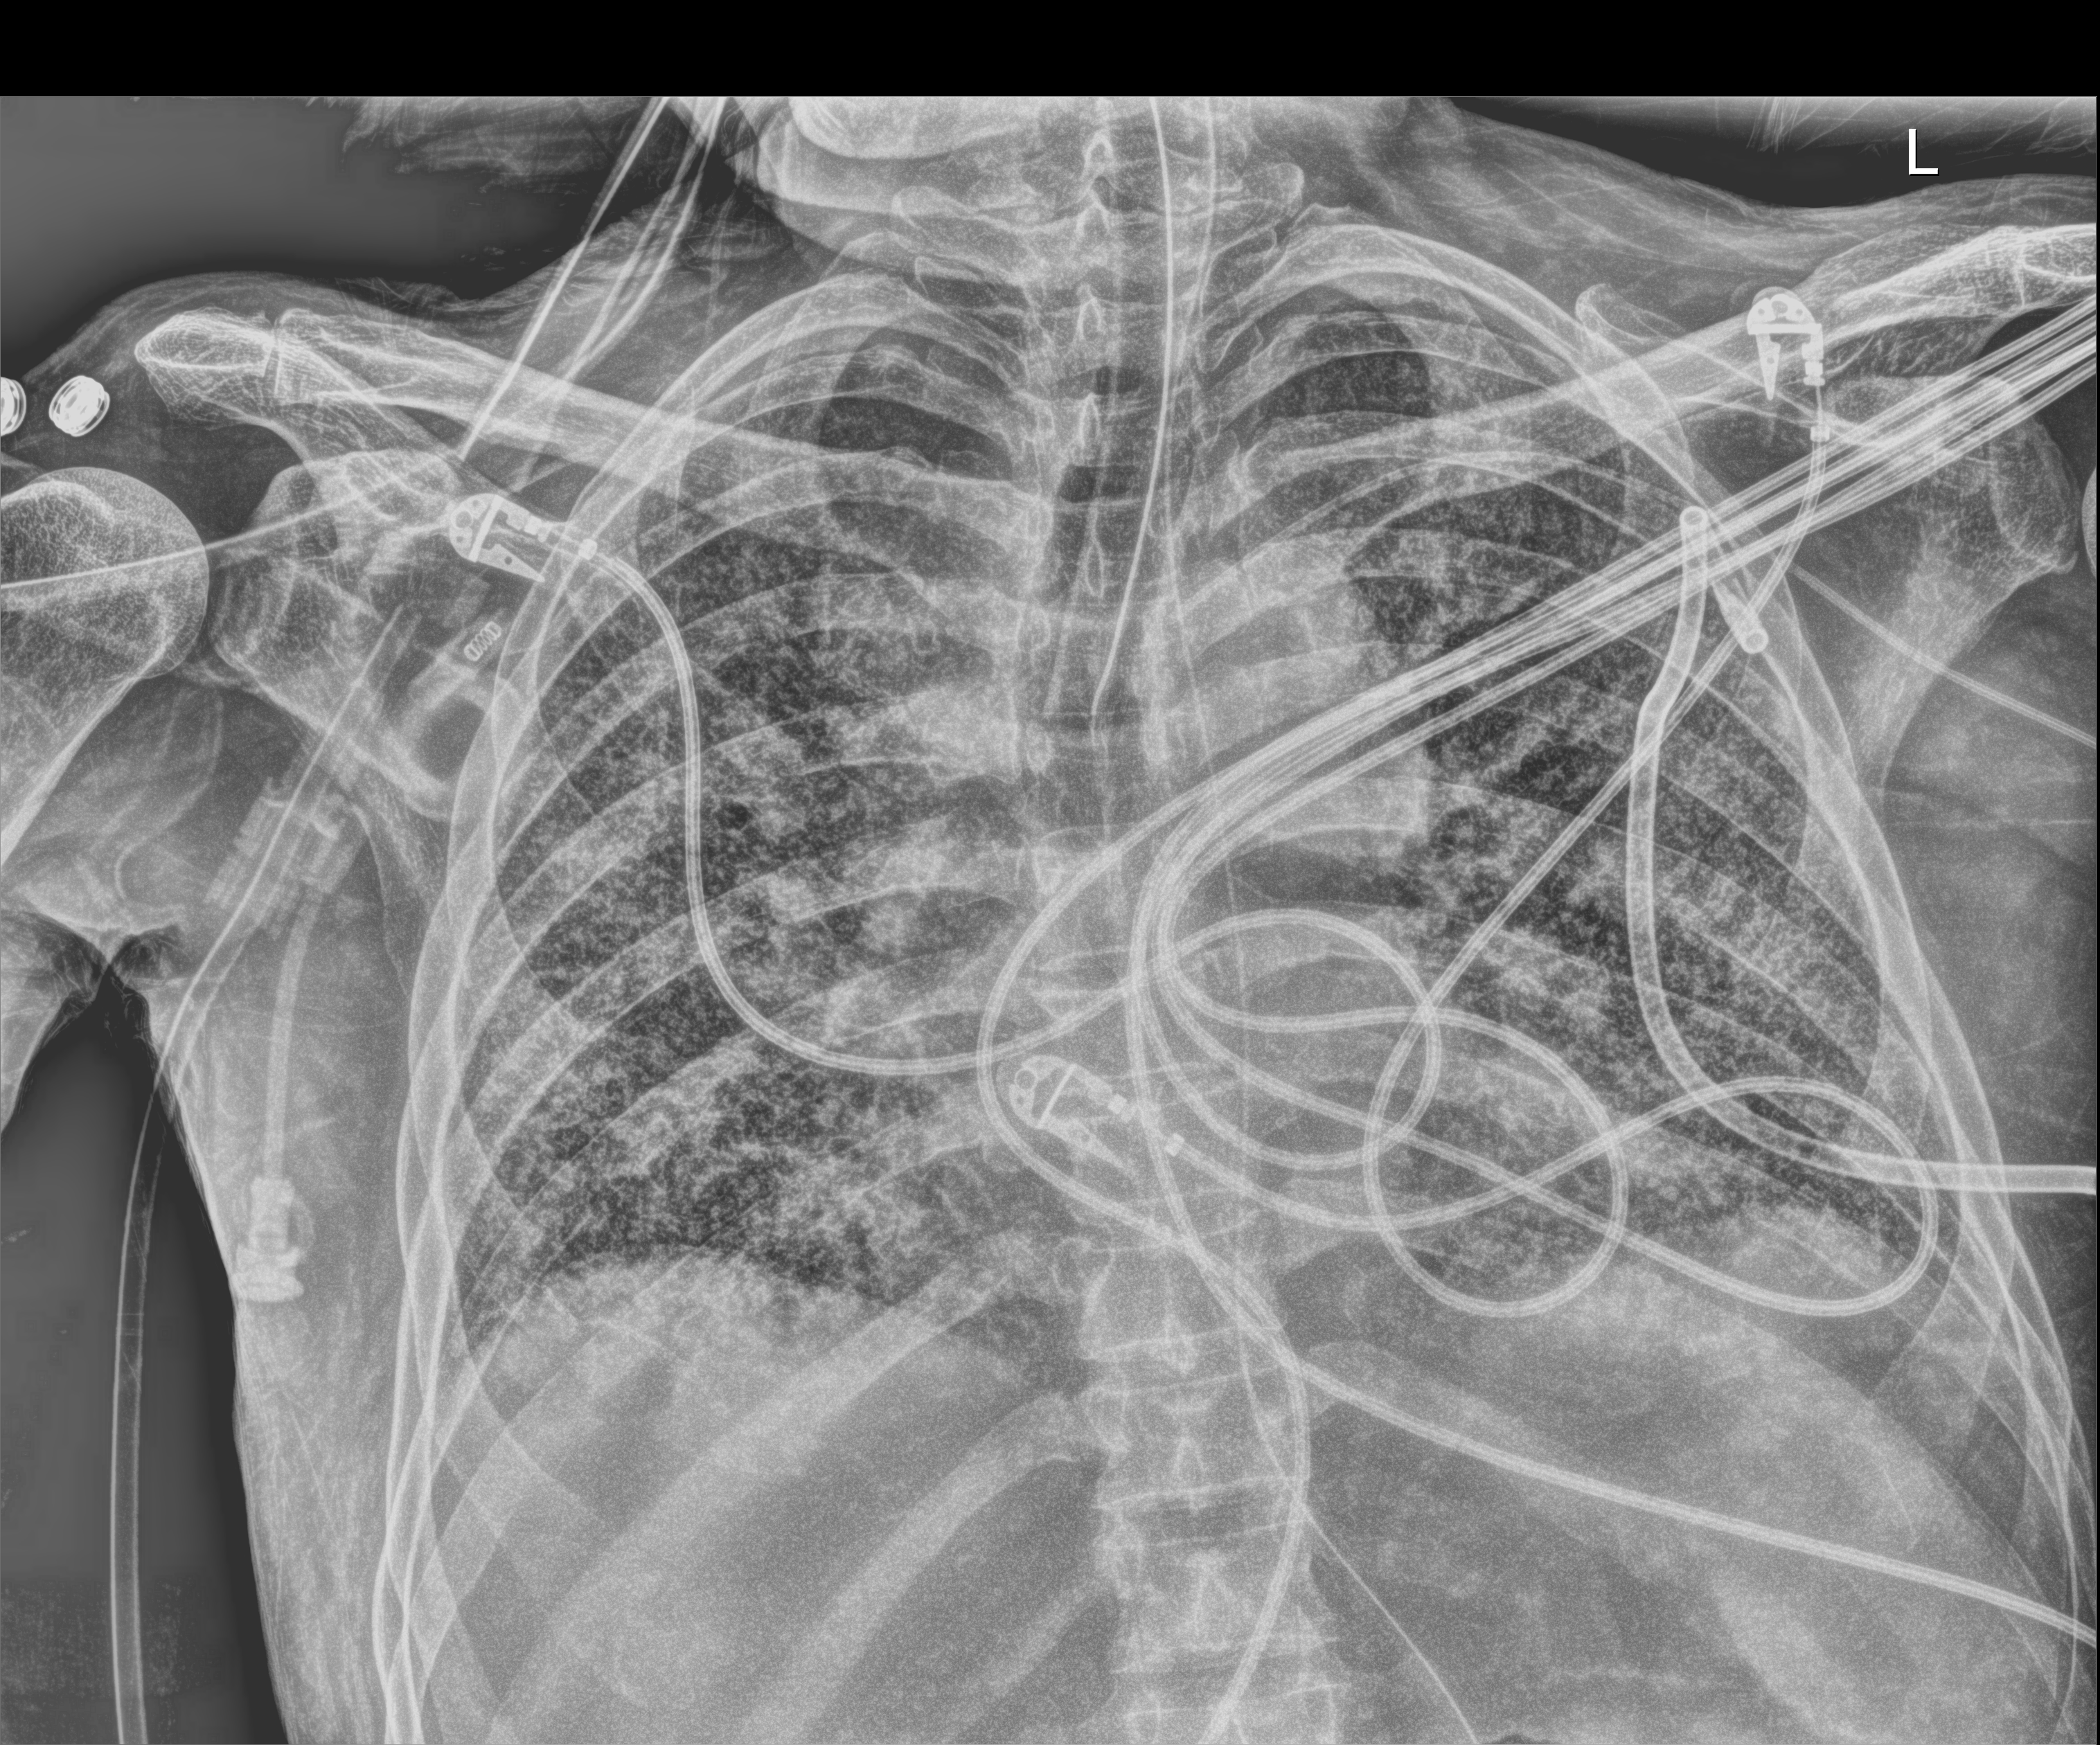
Chest radiograph (digital radiography), anteroposterior (AP) projection. Patient hospitalised with COVID-19; male, aged 60–74 years.
Hospital-stay facts (about this admission, not read from this image; timing relative to this image not recorded):
- admitted to intensive care during this hospital stay: yes
- mechanically ventilated during this hospital stay: yes
- length of hospital stay: 54 days